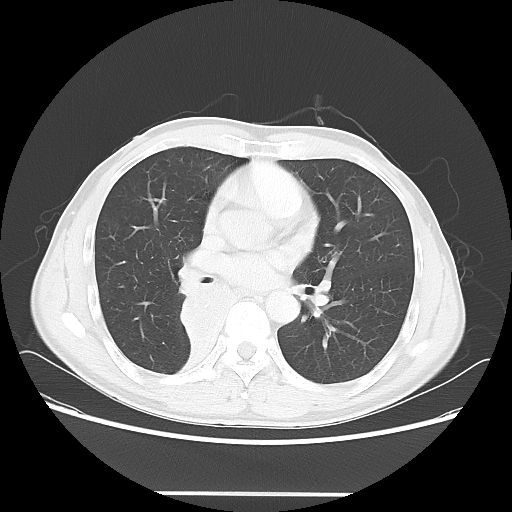
Chest CT, one axial slice. Slice 32 of 62 in the series (ordered by position). Reconstruction kernel LUNG. Lung window (W 1500 / L -600 HU). 5 mm slice thickness. 512 × 512 image matrix. Patient: male, 47 years. From the clinical record (not read from this slice): clinical TNM (as recorded): T2 N0 M0.
Structures marked on this image (bounding box drawn by a radiologist):
- lung tumour (recorded histology: squamous cell carcinoma): box from (x=178, y=280) to (x=254, y=369) px